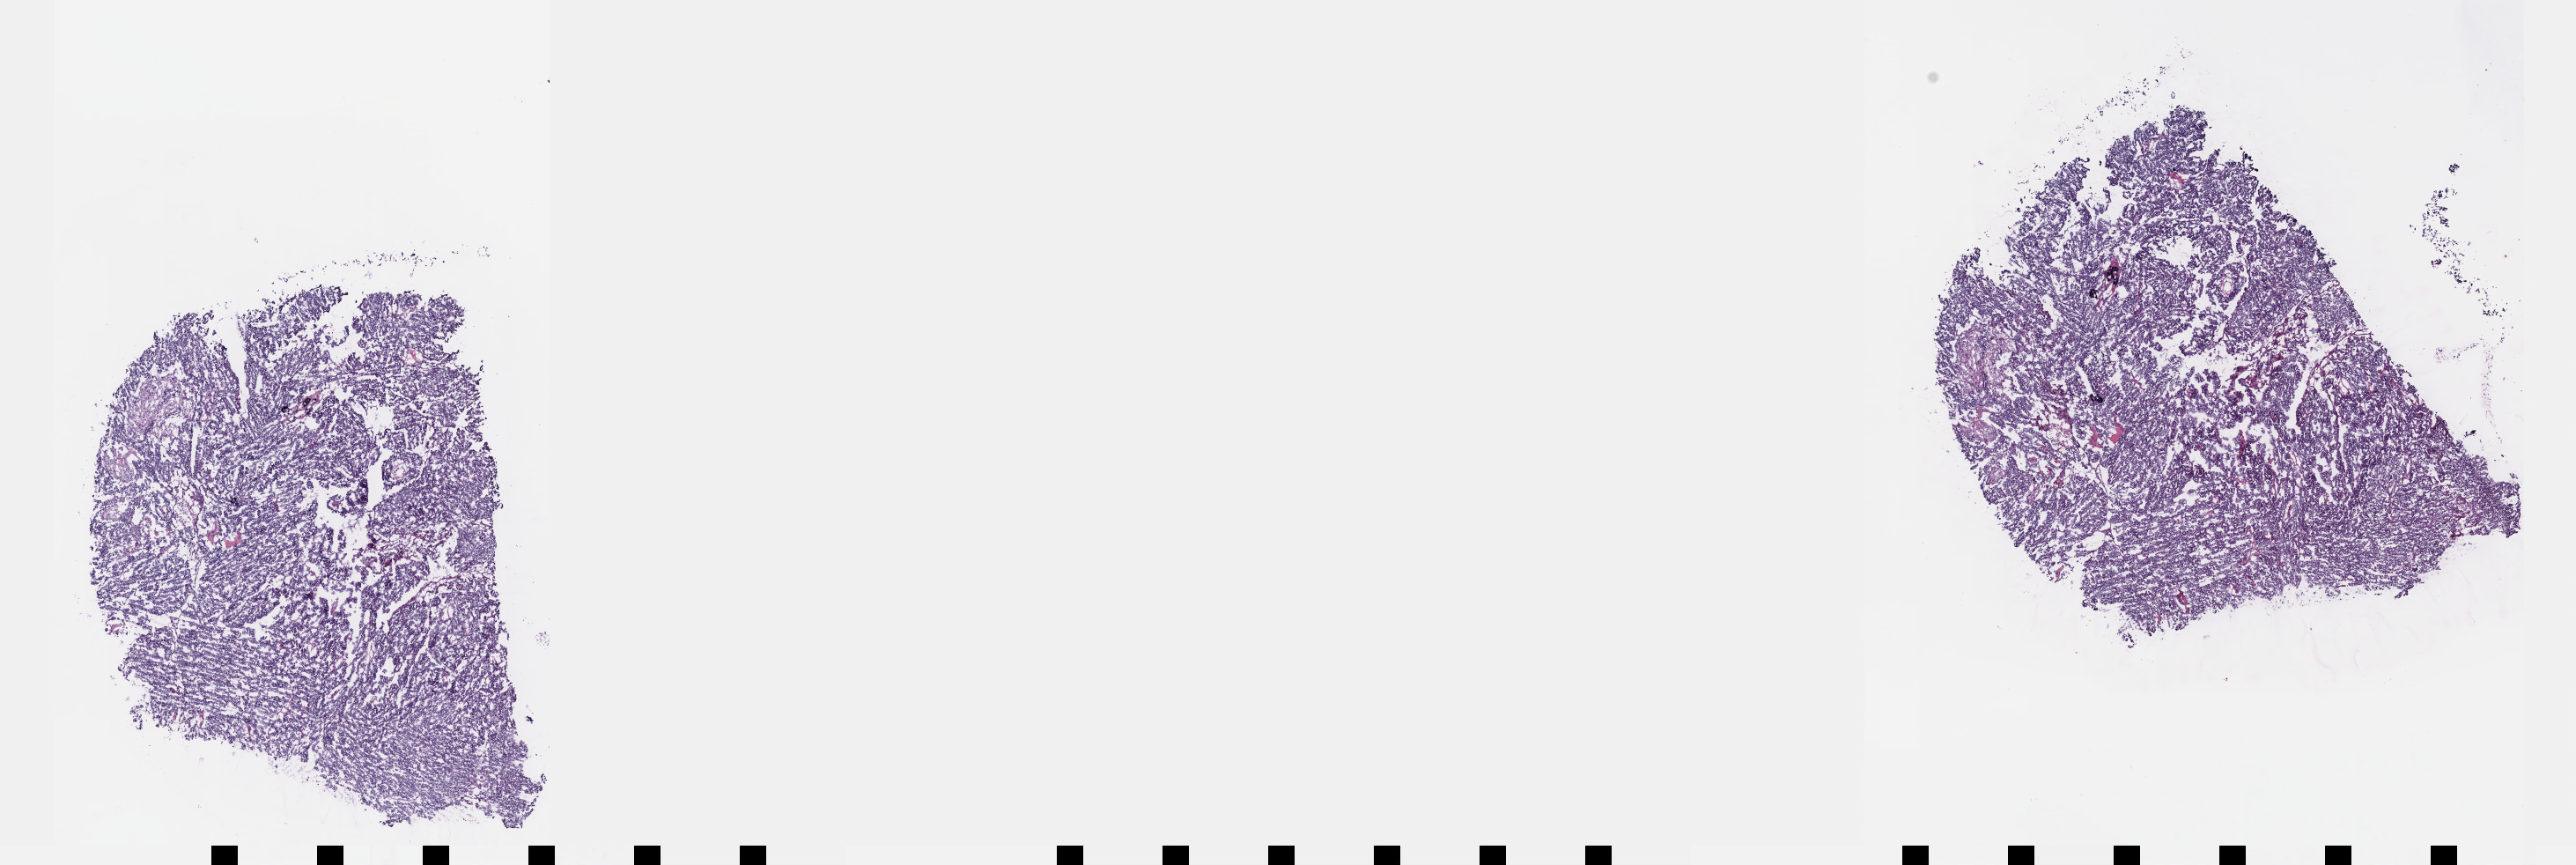
Whole-slide histology image, H&E-stained — shown as a low-resolution overview of the whole scanned area (about 23.6 x 7.9 mm); FFPE section; primary tumour sample from the ovary. Female patient; age at initial diagnosis 55 years. Histologic grade: GB (borderline).
FIGO stage: IV. Histologic diagnosis: Papillary serous cystadenocarcinoma.